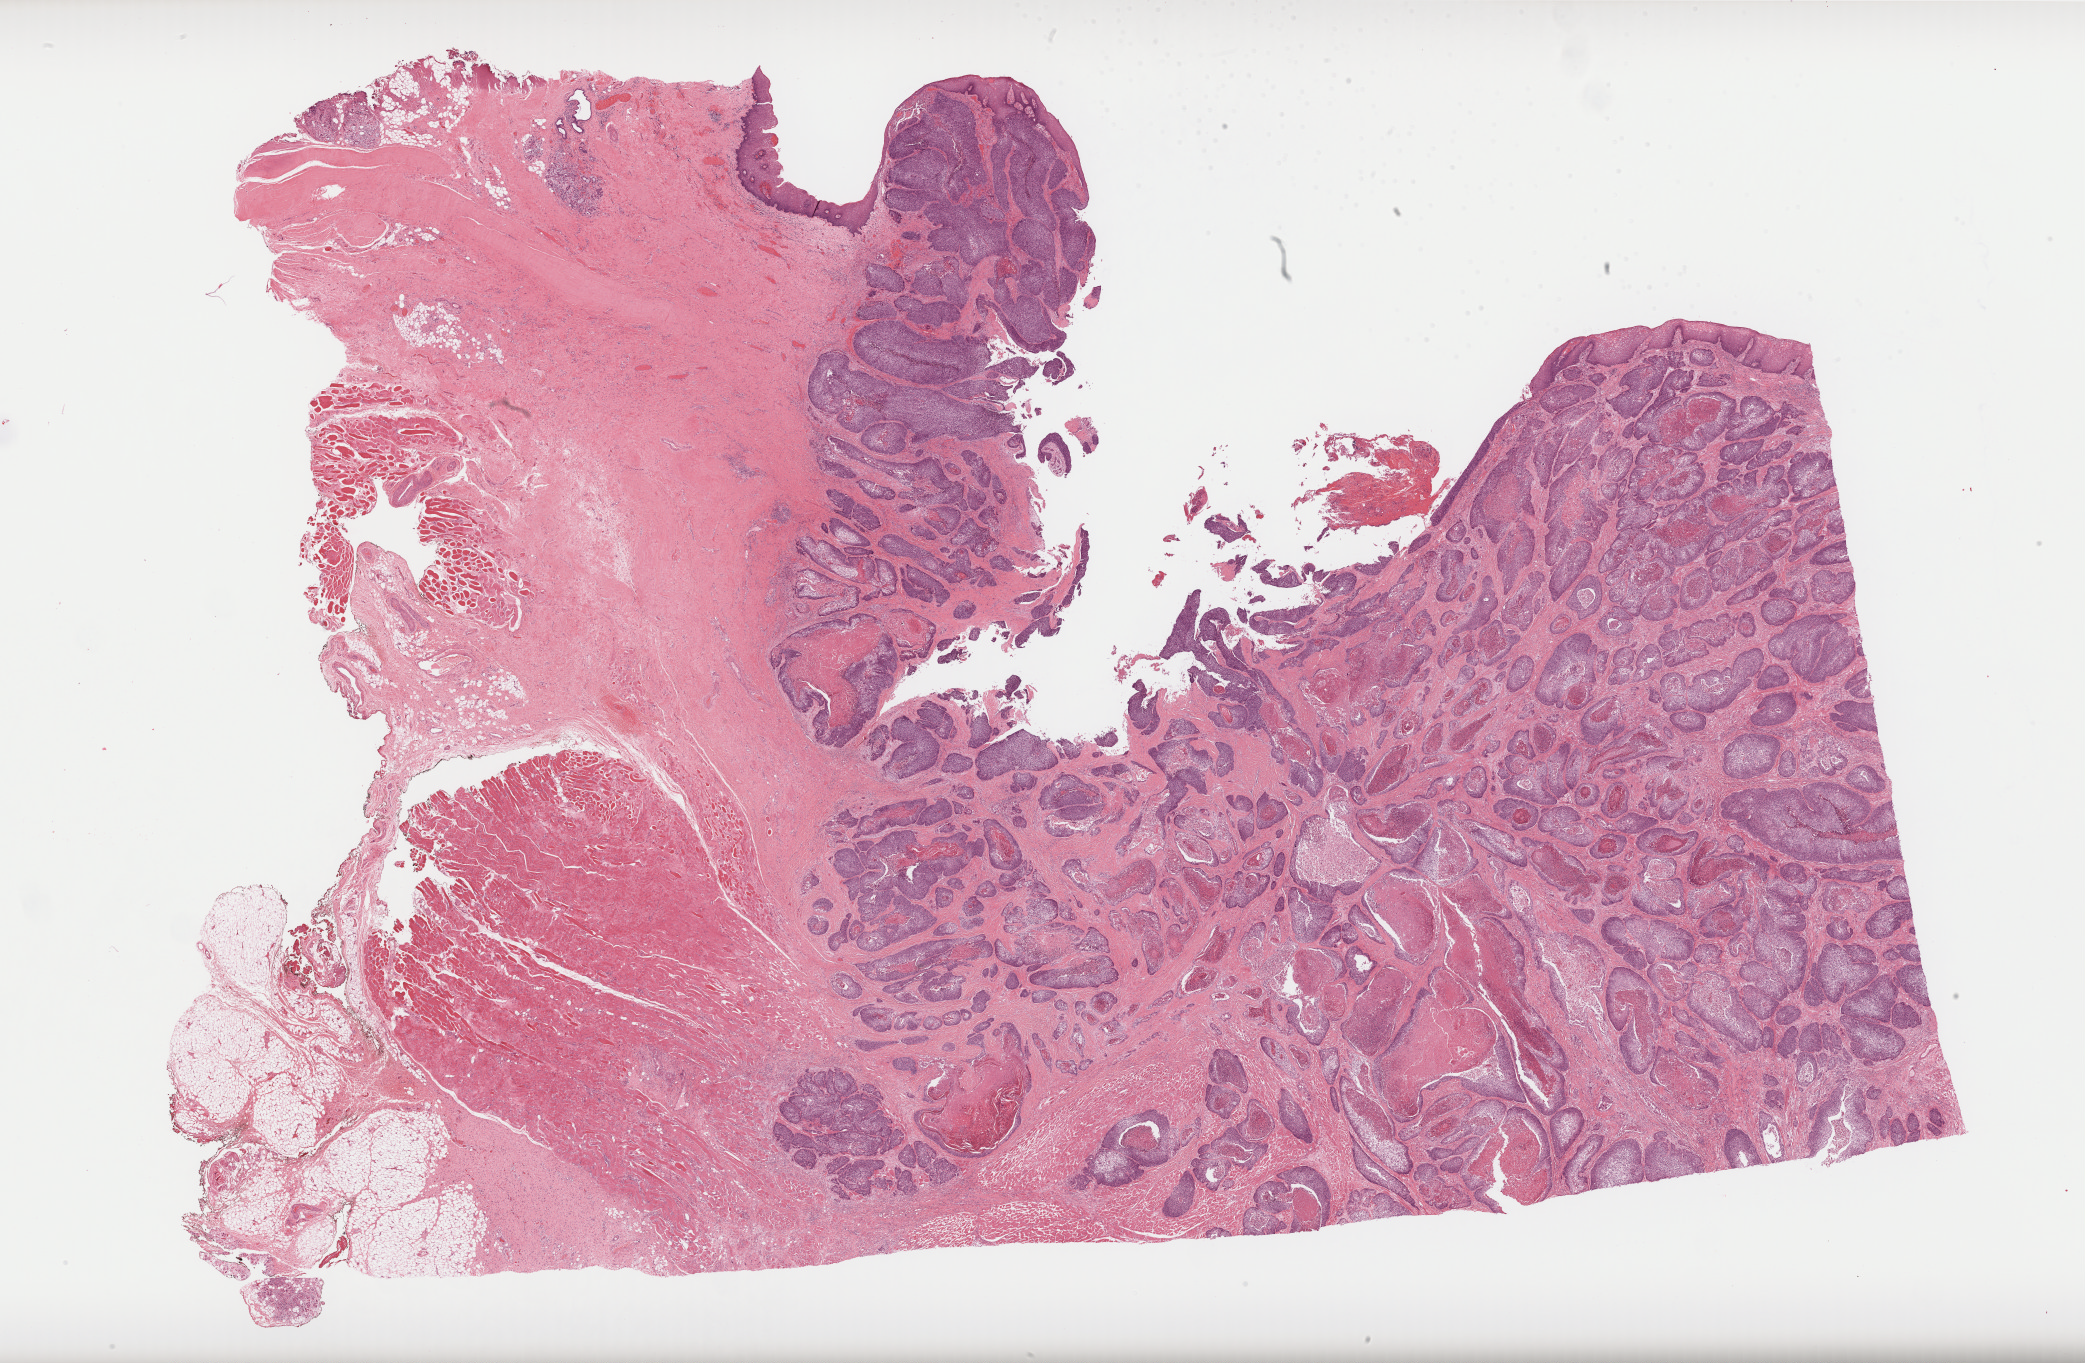
Digitized H&E-stained tissue section (whole slide), shown as a low-resolution overview of the whole scanned area (about 33.6 x 22.0 mm, from a 40x scan), formalin-fixed paraffin-embedded (FFPE) diagnostic section, head and neck, primary tumour sample. Male, age 65 years at initial diagnosis. Histologic grade: G2 (moderately differentiated).
AJCC pathologic stage: III. Lymph nodes positive (case pathology): 0 of 25 examined. TNM: T3 N0. Histologic diagnosis: Squamous cell carcinoma, NOS. Laterality: left.